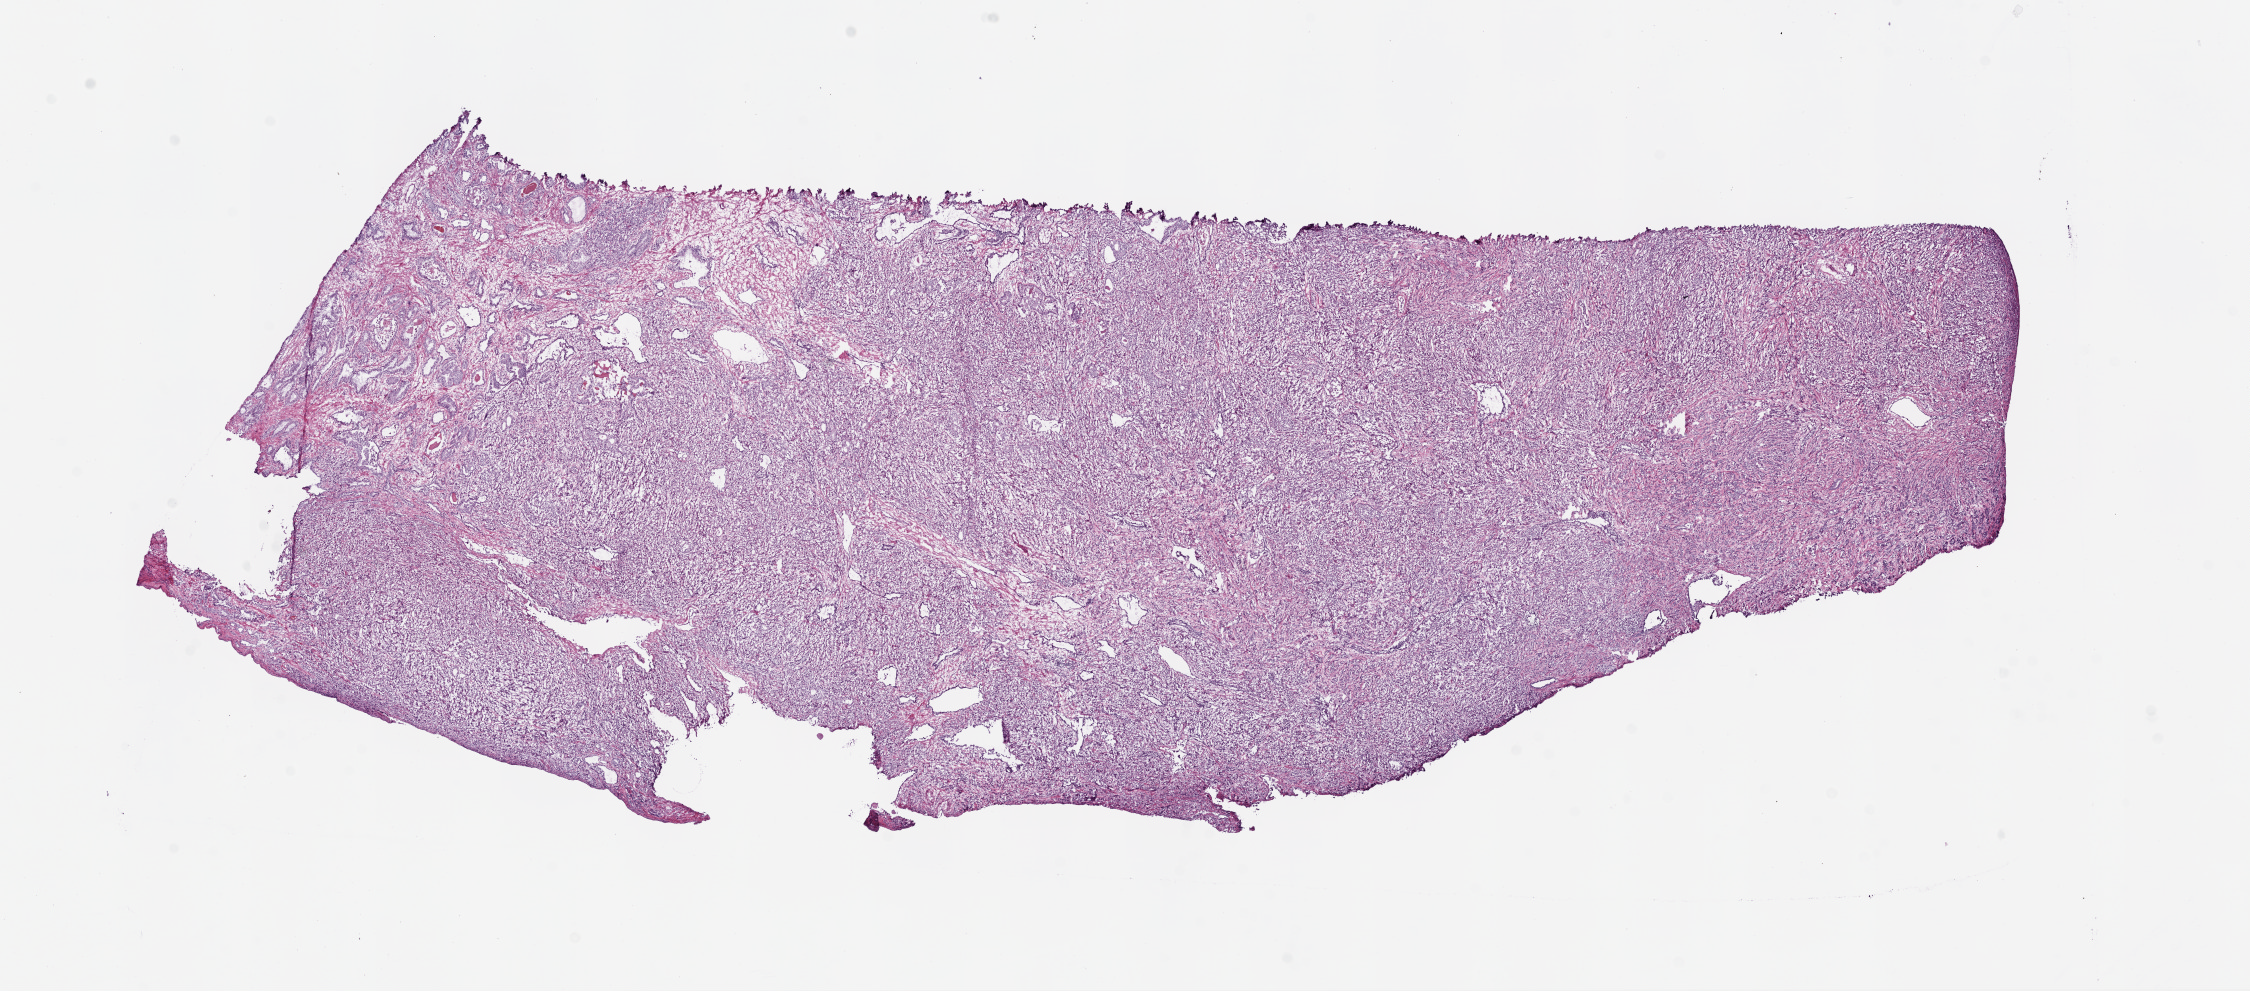
H&E-stained whole-slide image — shown as a low-resolution overview of the whole scanned area (about 18.1 x 8.0 mm, acquisition: 20x scan), frozen section from the top of the tissue portion, sample: primary tumour, prostate. Patient: male, age at initial diagnosis 56 years. Gleason score: 8 (4+4). Slide review estimates, as recorded: tumour cells 80%, tumour nuclei 85%, normal cells 5%, stromal cells 15%, necrosis 0%. Inflammatory infiltration, as recorded: lymphocyte infiltration 2%, monocyte infiltration 0%, neutrophil infiltration 0%.
- histologic diagnosis: Acinar cell carcinoma (prostate gland)
- lymph nodes positive (case pathology): 1 of 27 examined